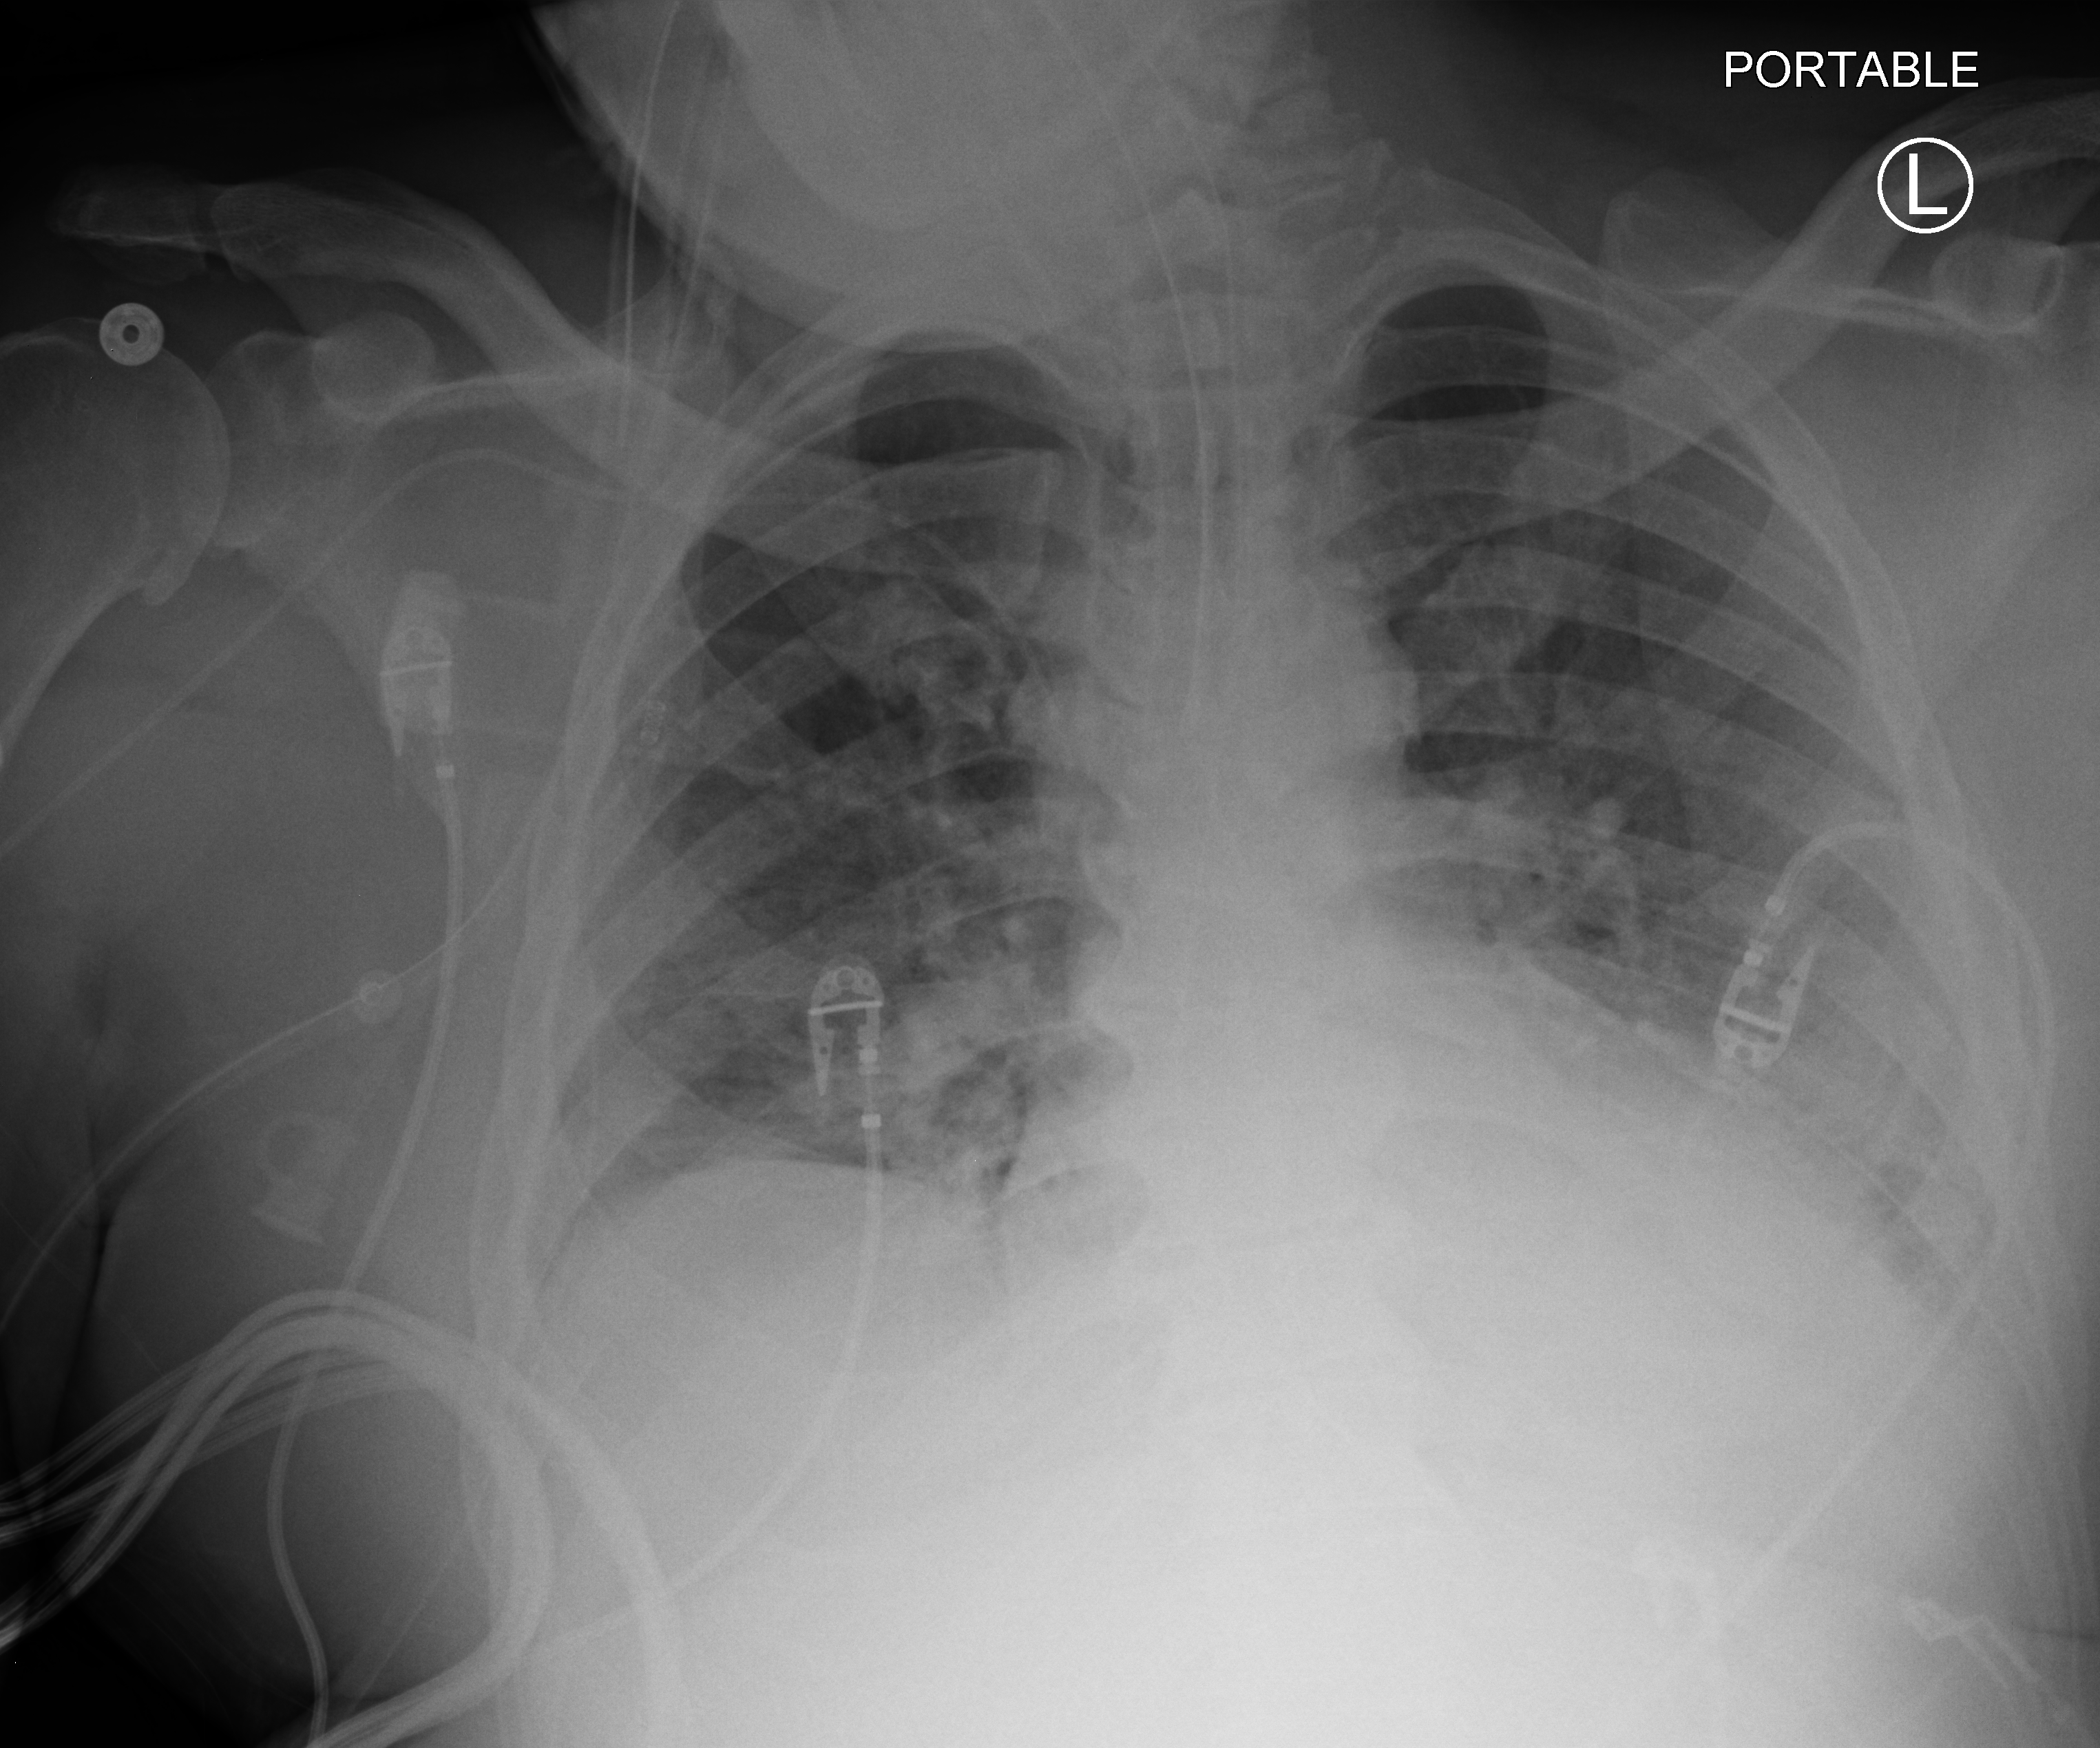
Chest X-ray (portable), anteroposterior (AP) projection. Male patient hospitalised with COVID-19, age 18–59 years.
From the hospital-stay record, not from the radiograph (when in the stay this image was taken is not recorded):
- length of hospital stay: 41 days
- mechanically ventilated during this hospital stay: yes